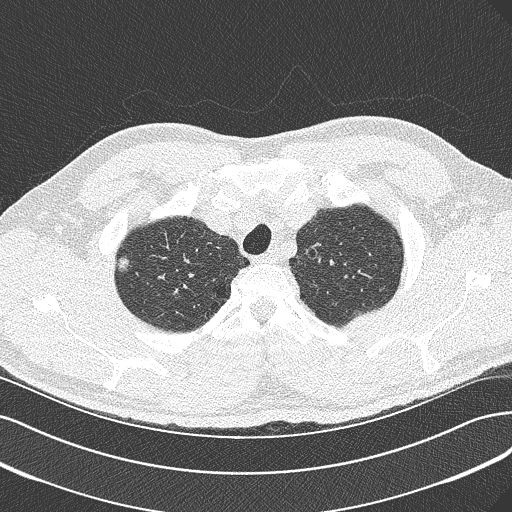
Chest CT (low-dose screening protocol), one axial image. First (baseline) screen. Lung window (W 1500 / L -600 HU). 1 mm slice thickness. Slice 44 of 342 in the series. 512 × 512 image matrix, field of view 360 × 360 mm. Male, age 56 years at enrolment.
Lesion marked by an expert reader, bounding box (x1, y1, x2, y2) in pixels: (105, 248, 145, 286). Screening reader's record for this exam (one nodule recorded; not confirmed to be the boxed lesion): non-calcified nodule or mass ≥4 mm, right upper lobe, 10 × 7 mm, spiculated (stellate) margins, soft tissue attenuation. Later outcome: lung cancer diagnosed 517 days after this screen — bronchiolo-alveolar carcinoma, non-mucinous, right upper lobe, moderately differentiated (G2), stage IIIB (AJCC 6th edition), 10 mm at pathology.